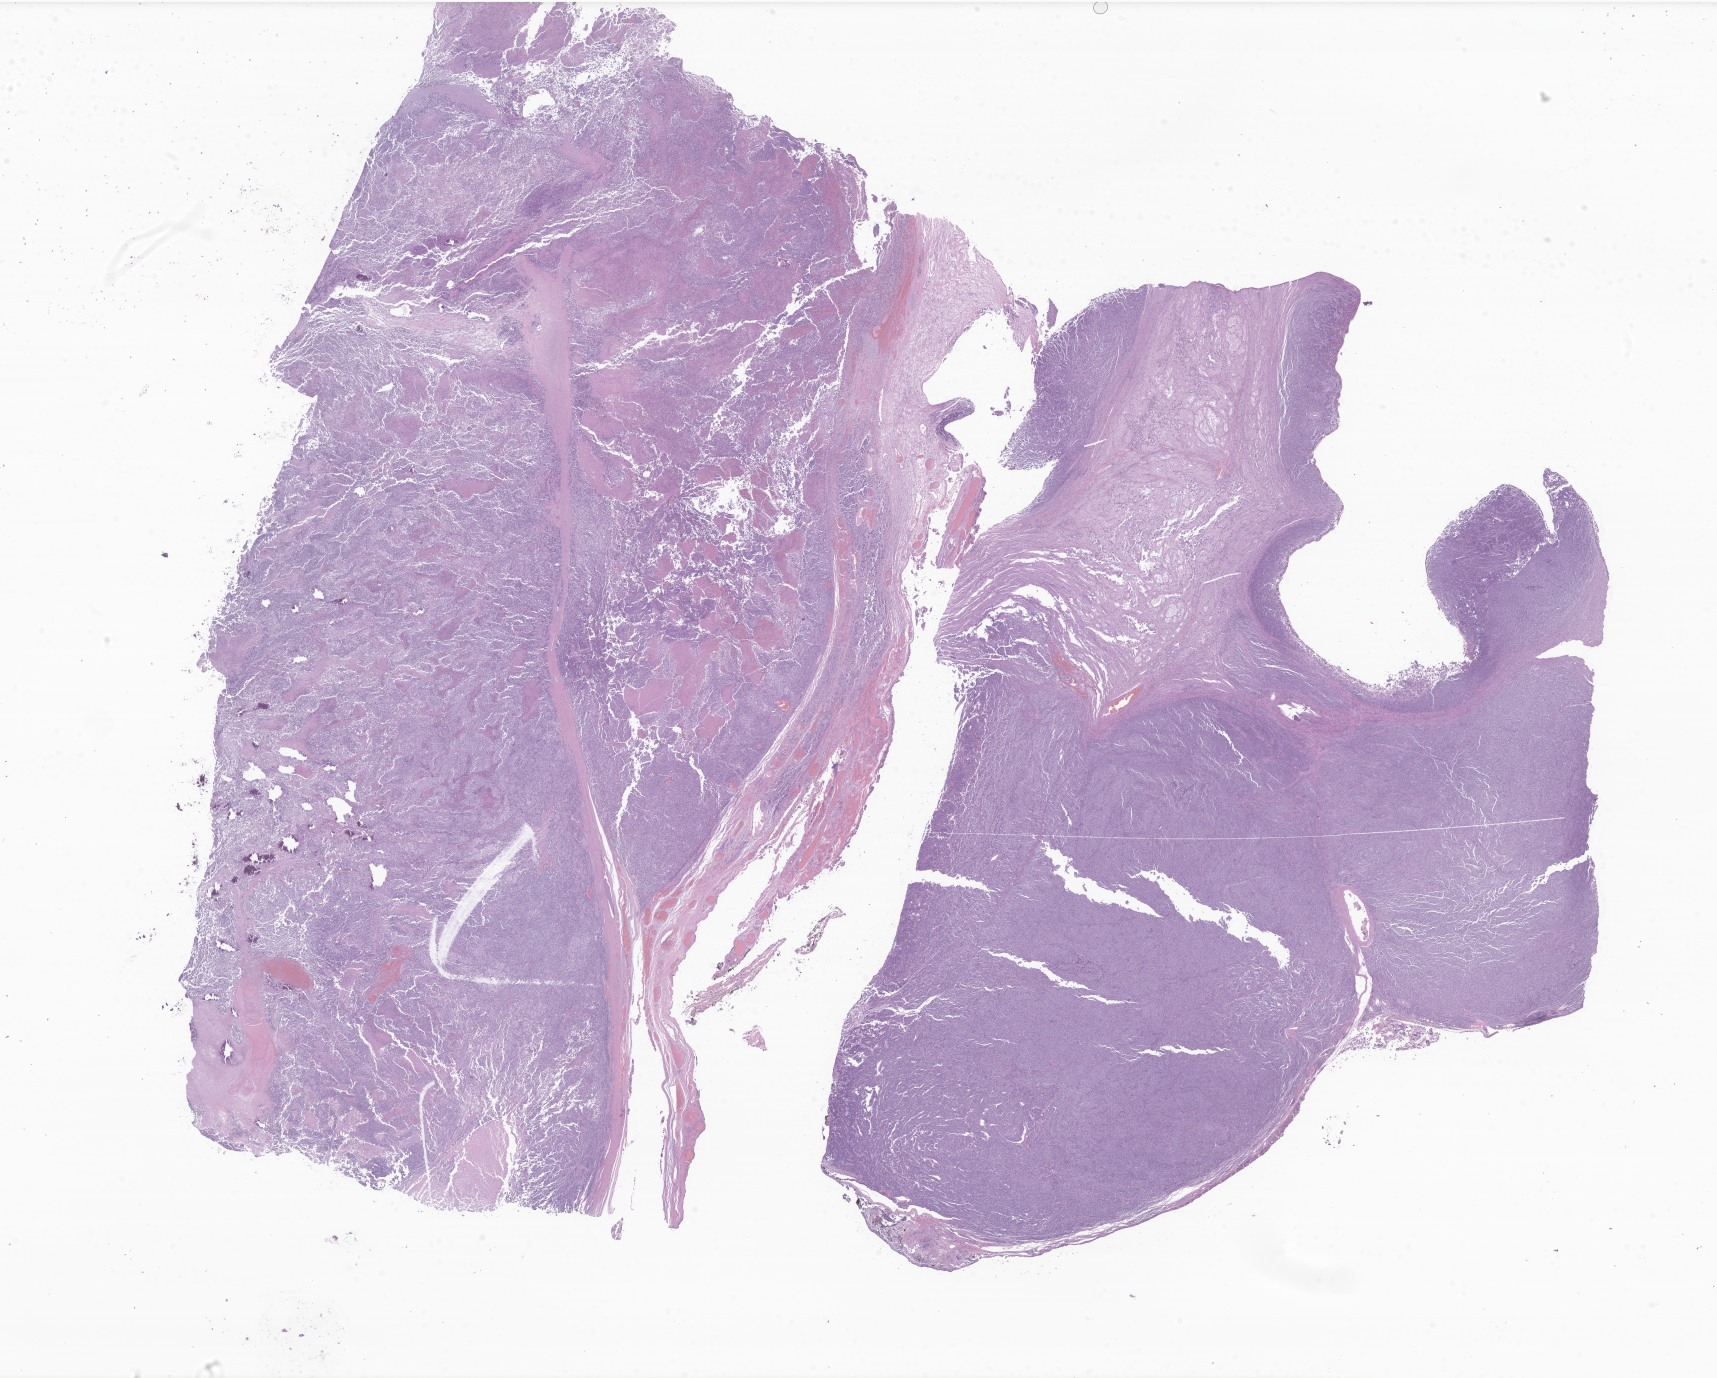
Haematoxylin and eosin whole-slide image of tumor tissue from the retroperitoneum — shown as a low-resolution overview of the whole scanned area (about 29.0 x 23.2 mm); formalin-fixed, paraffin-embedded (FFPE) tissue. Male patient, age 68 months (5 years 8 months).
Diagnosis (ICD-O-3 morphology term): Pheochromocytoma, NOS.